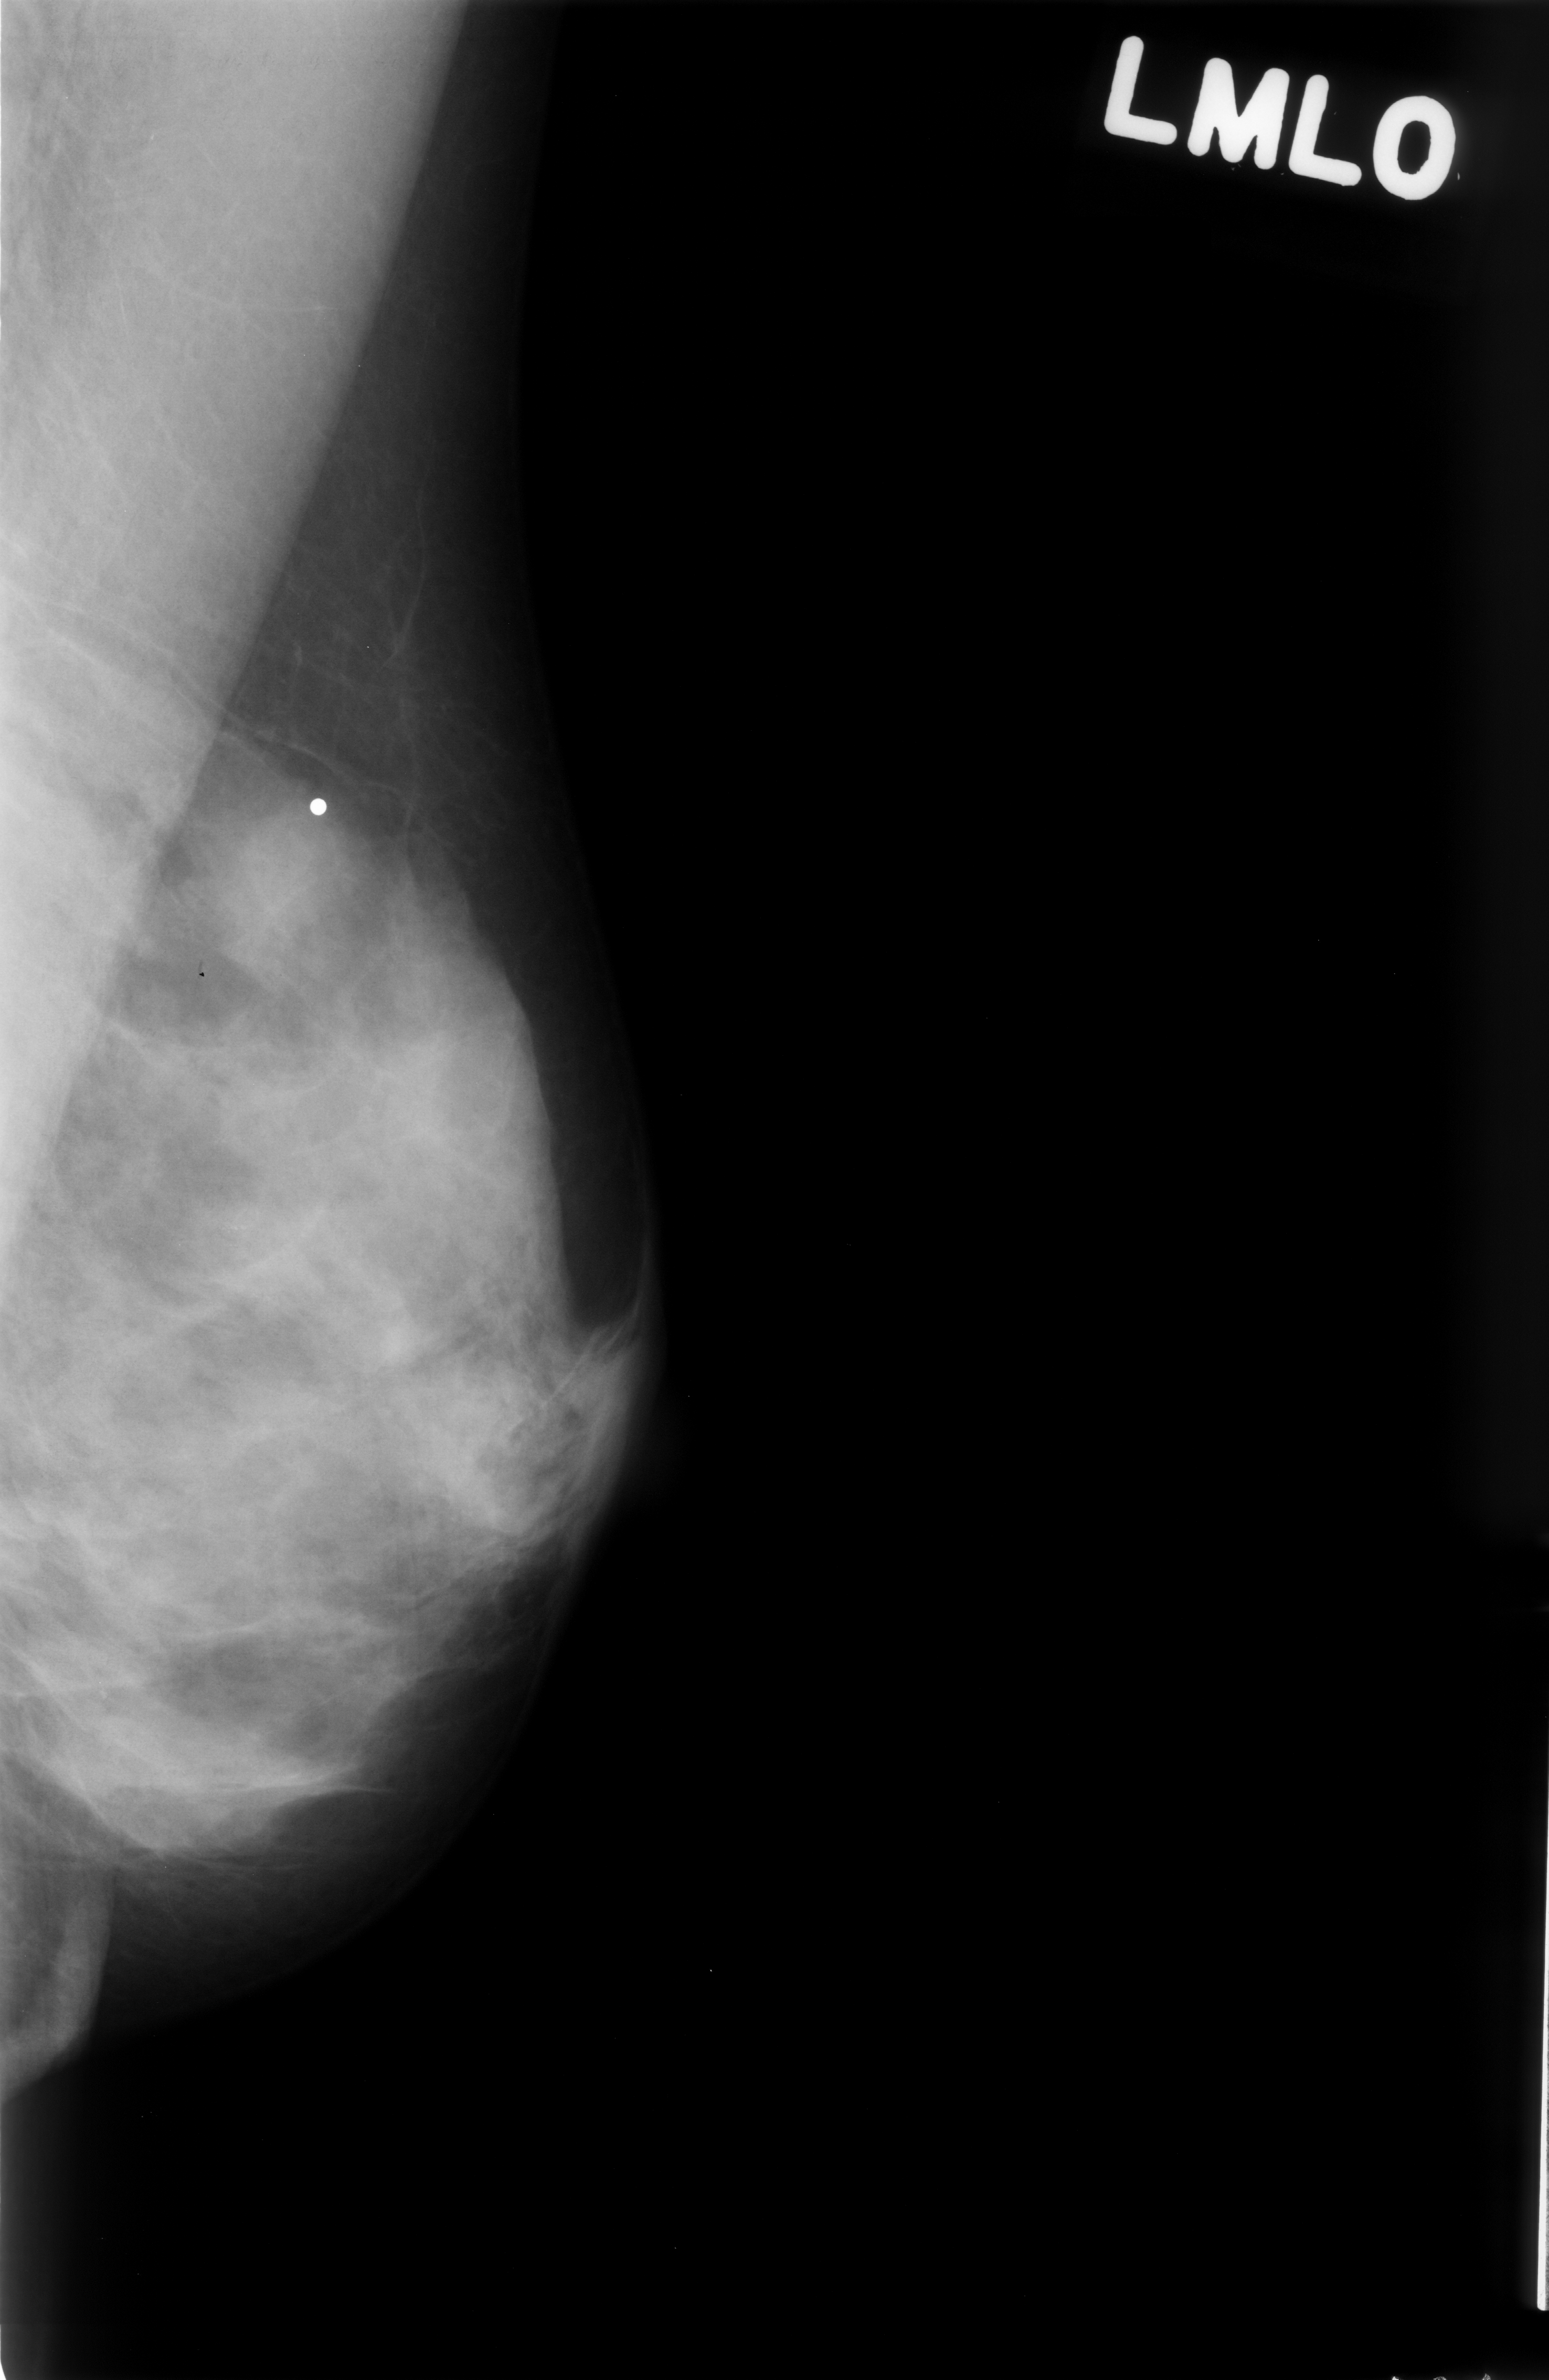
Digitized screen-film mammogram. Left breast. Mediolateral oblique (MLO) view. BI-RADS breast density category 4 (scale 1–4). 1549 × 2380 image matrix.
Marked abnormalities (boxes around the expert regions of interest):
- calcifications, morphology amorphous, distribution clustered; BI-RADS assessment category 4; pathology result (as recorded, not read from the image): benign: bounding box <176,1171,362,1357> (left, top, right, bottom; pixels)